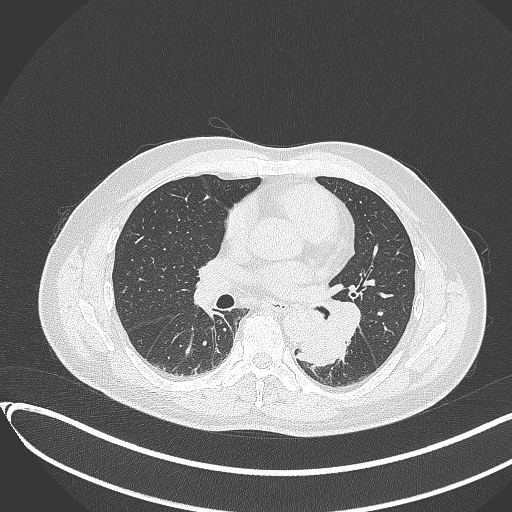
Chest CT, one axial slice; slice 178 of 417 in the series (ordered by position); reconstruction kernel B70f; lung window (W 1500 / L -600 HU); 1 mm slice thickness; 512 × 512 image matrix. Patient: male, 54 years. Case-level facts recorded for this patient, not image findings: clinical TNM (as recorded): T3 N0 M0.
Annotated regions visible in this slice (rectangle marked by the reading radiologist):
- lung tumour (recorded histology: squamous cell carcinoma): box from (x=284, y=311) to (x=348, y=368) px